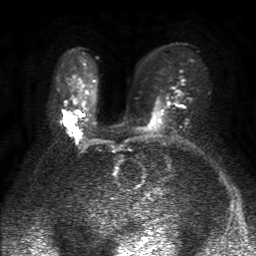
Breast MRI, one axial slice; slice 29 of 50 in the series (ordered by position); diffusion-weighted series; image 2 of 4 stored at this slice position (different b-values; order by instance number); 1.5 T; 4 mm slice thickness; 256 × 256 image matrix, field of view 320 × 320 mm. Female patient.
Structures marked on this image (outlined manually by an expert reader):
- tumour on diffusion-weighted imaging: bounding box [x1, y1, x2, y2] px = [69, 124, 73, 129]